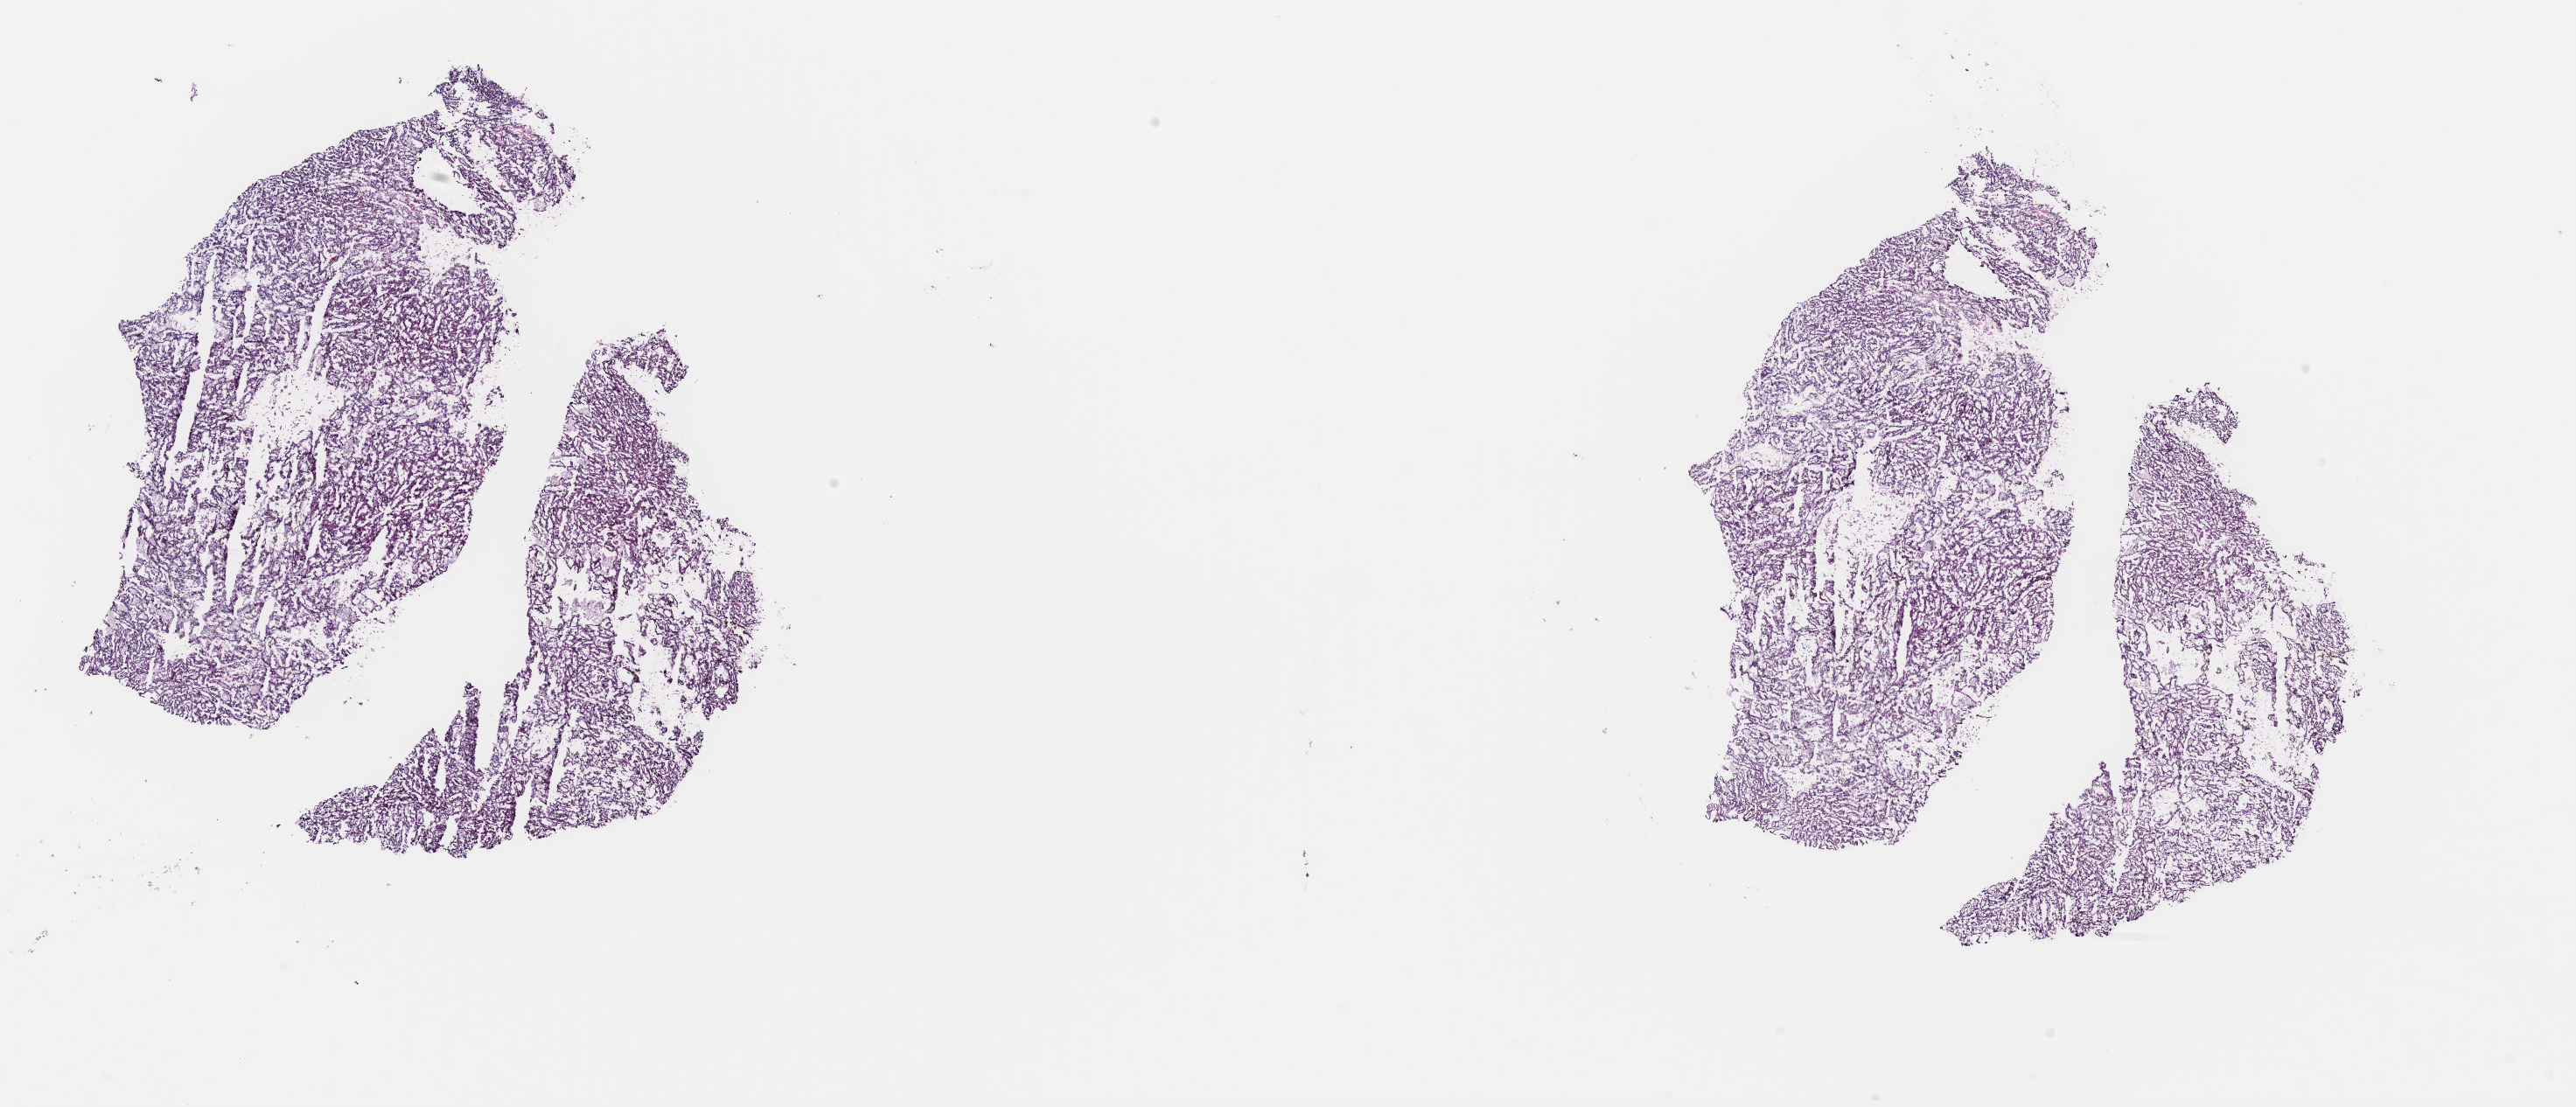
Whole-slide histology image, H&E, low-resolution overview of the scanned area, about 23.3 x 10.0 mm (slide scanned at 40x). Frozen section from the top of the tissue portion. Kidney, primary tumour sample. Male patient; age at initial diagnosis 63 years.
Diagnosis: Papillary adenocarcinoma, NOS.